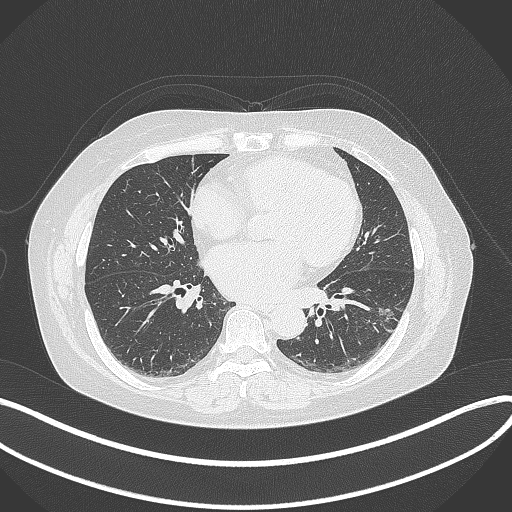
Chest CT, one axial slice. Position 155 of 373 along the scan axis. Reconstruction kernel B70f. Lung window (W 1500 / L -600 HU). 1 mm slice thickness. 512 × 512 image matrix, field of view 400 × 400 mm. Patient: female, 67 years. Case-level facts recorded for this patient, not image findings: clinical TNM (as recorded): T1c N0 M0; histopathological grade: G2.
Outlined on this slice (rectangle marked by the reading radiologist):
- lung tumour (recorded histology: adenocarcinoma): bounding box <369,300,408,331> (left, top, right, bottom; pixels)